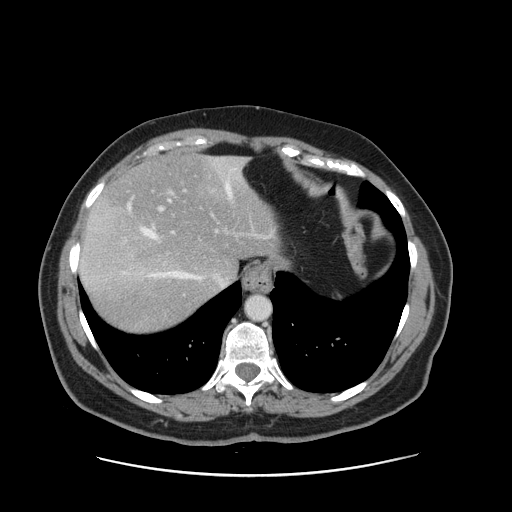
Contrast-enhanced abdominal CT, one axial slice. Slice 123 of 161 in the series (ordered by position). 120 kVp. Intravenous contrast given. Soft-tissue window (W 400 / L 40 HU). 2.5 mm slice thickness. 512 × 512 image matrix. Female patient, age 62 years. From the clinical record (not read from this slice): diagnosis: colorectal cancer liver metastases, imaged before liver resection; multiple liver metastases: no; largest metastasis: 2.5 cm; chemotherapy before resection: yes.
Annotated regions visible in this slice (manually delineated by an expert):
- hepatic veins: bounding box [x1, y1, x2, y2] px = [123, 159, 244, 286]
- liver: [80, 156, 280, 333]
- planned liver remnant (the part of the liver to remain after resection): [96, 156, 279, 278]
- portal vein (with intrahepatic branches): [157, 189, 271, 238]